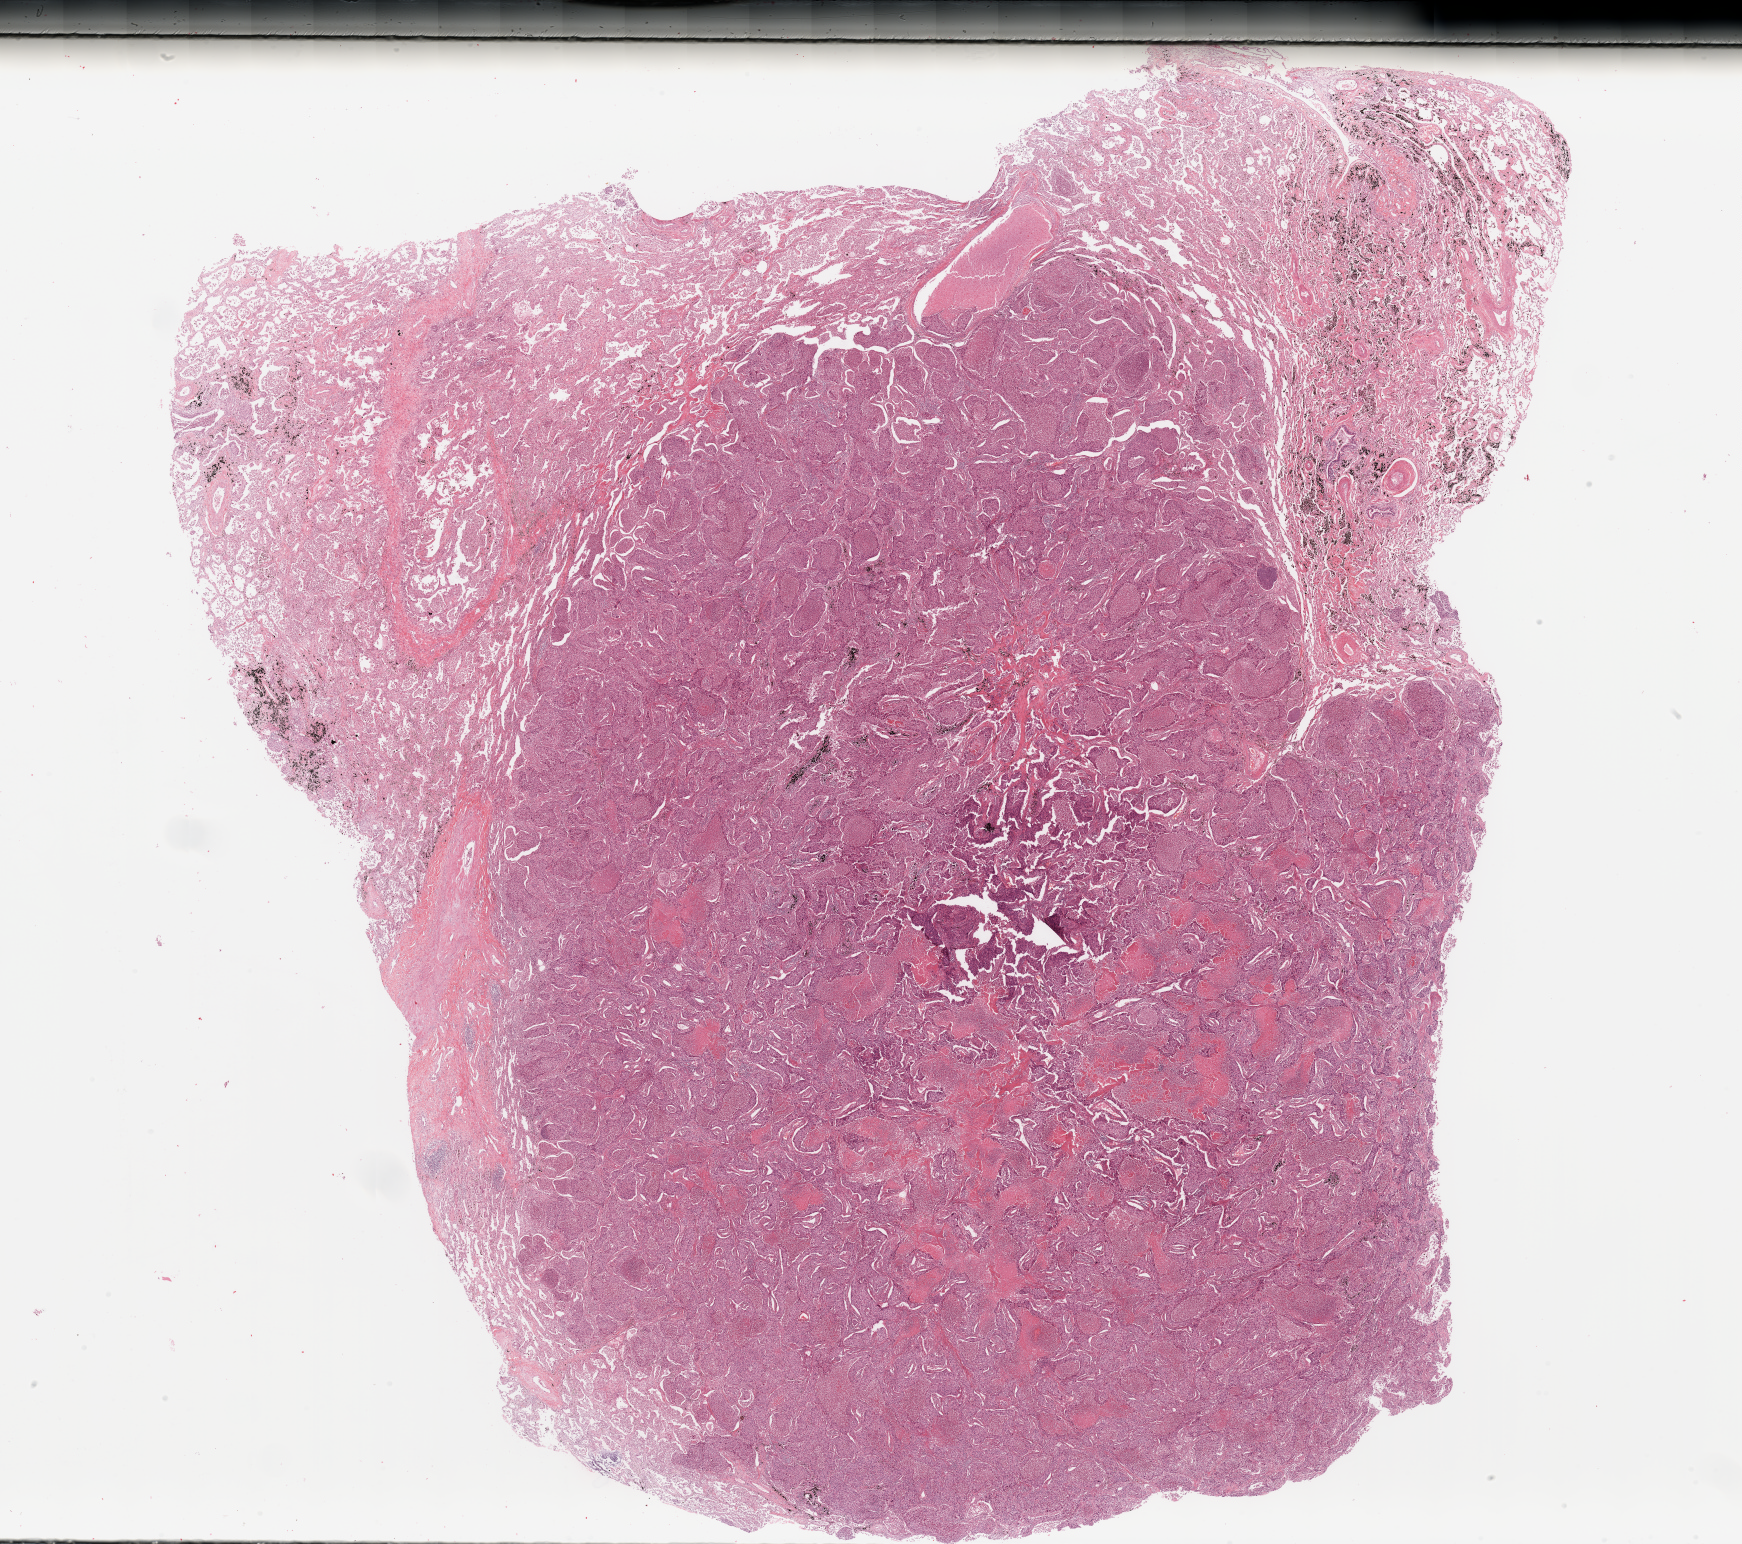
Hematoxylin and eosin (H&E) stained whole-slide image — a low-resolution overview of the entire scanned area, about 27.6 x 24.4 mm (acquisition: 20x scan); tumour tissue sample, lung. Male, 65 y/o. Histologic grade: G3 (poorly differentiated).
Histologic diagnosis: Squamous cell carcinoma, NOS. AJCC pathologic stage: IB.